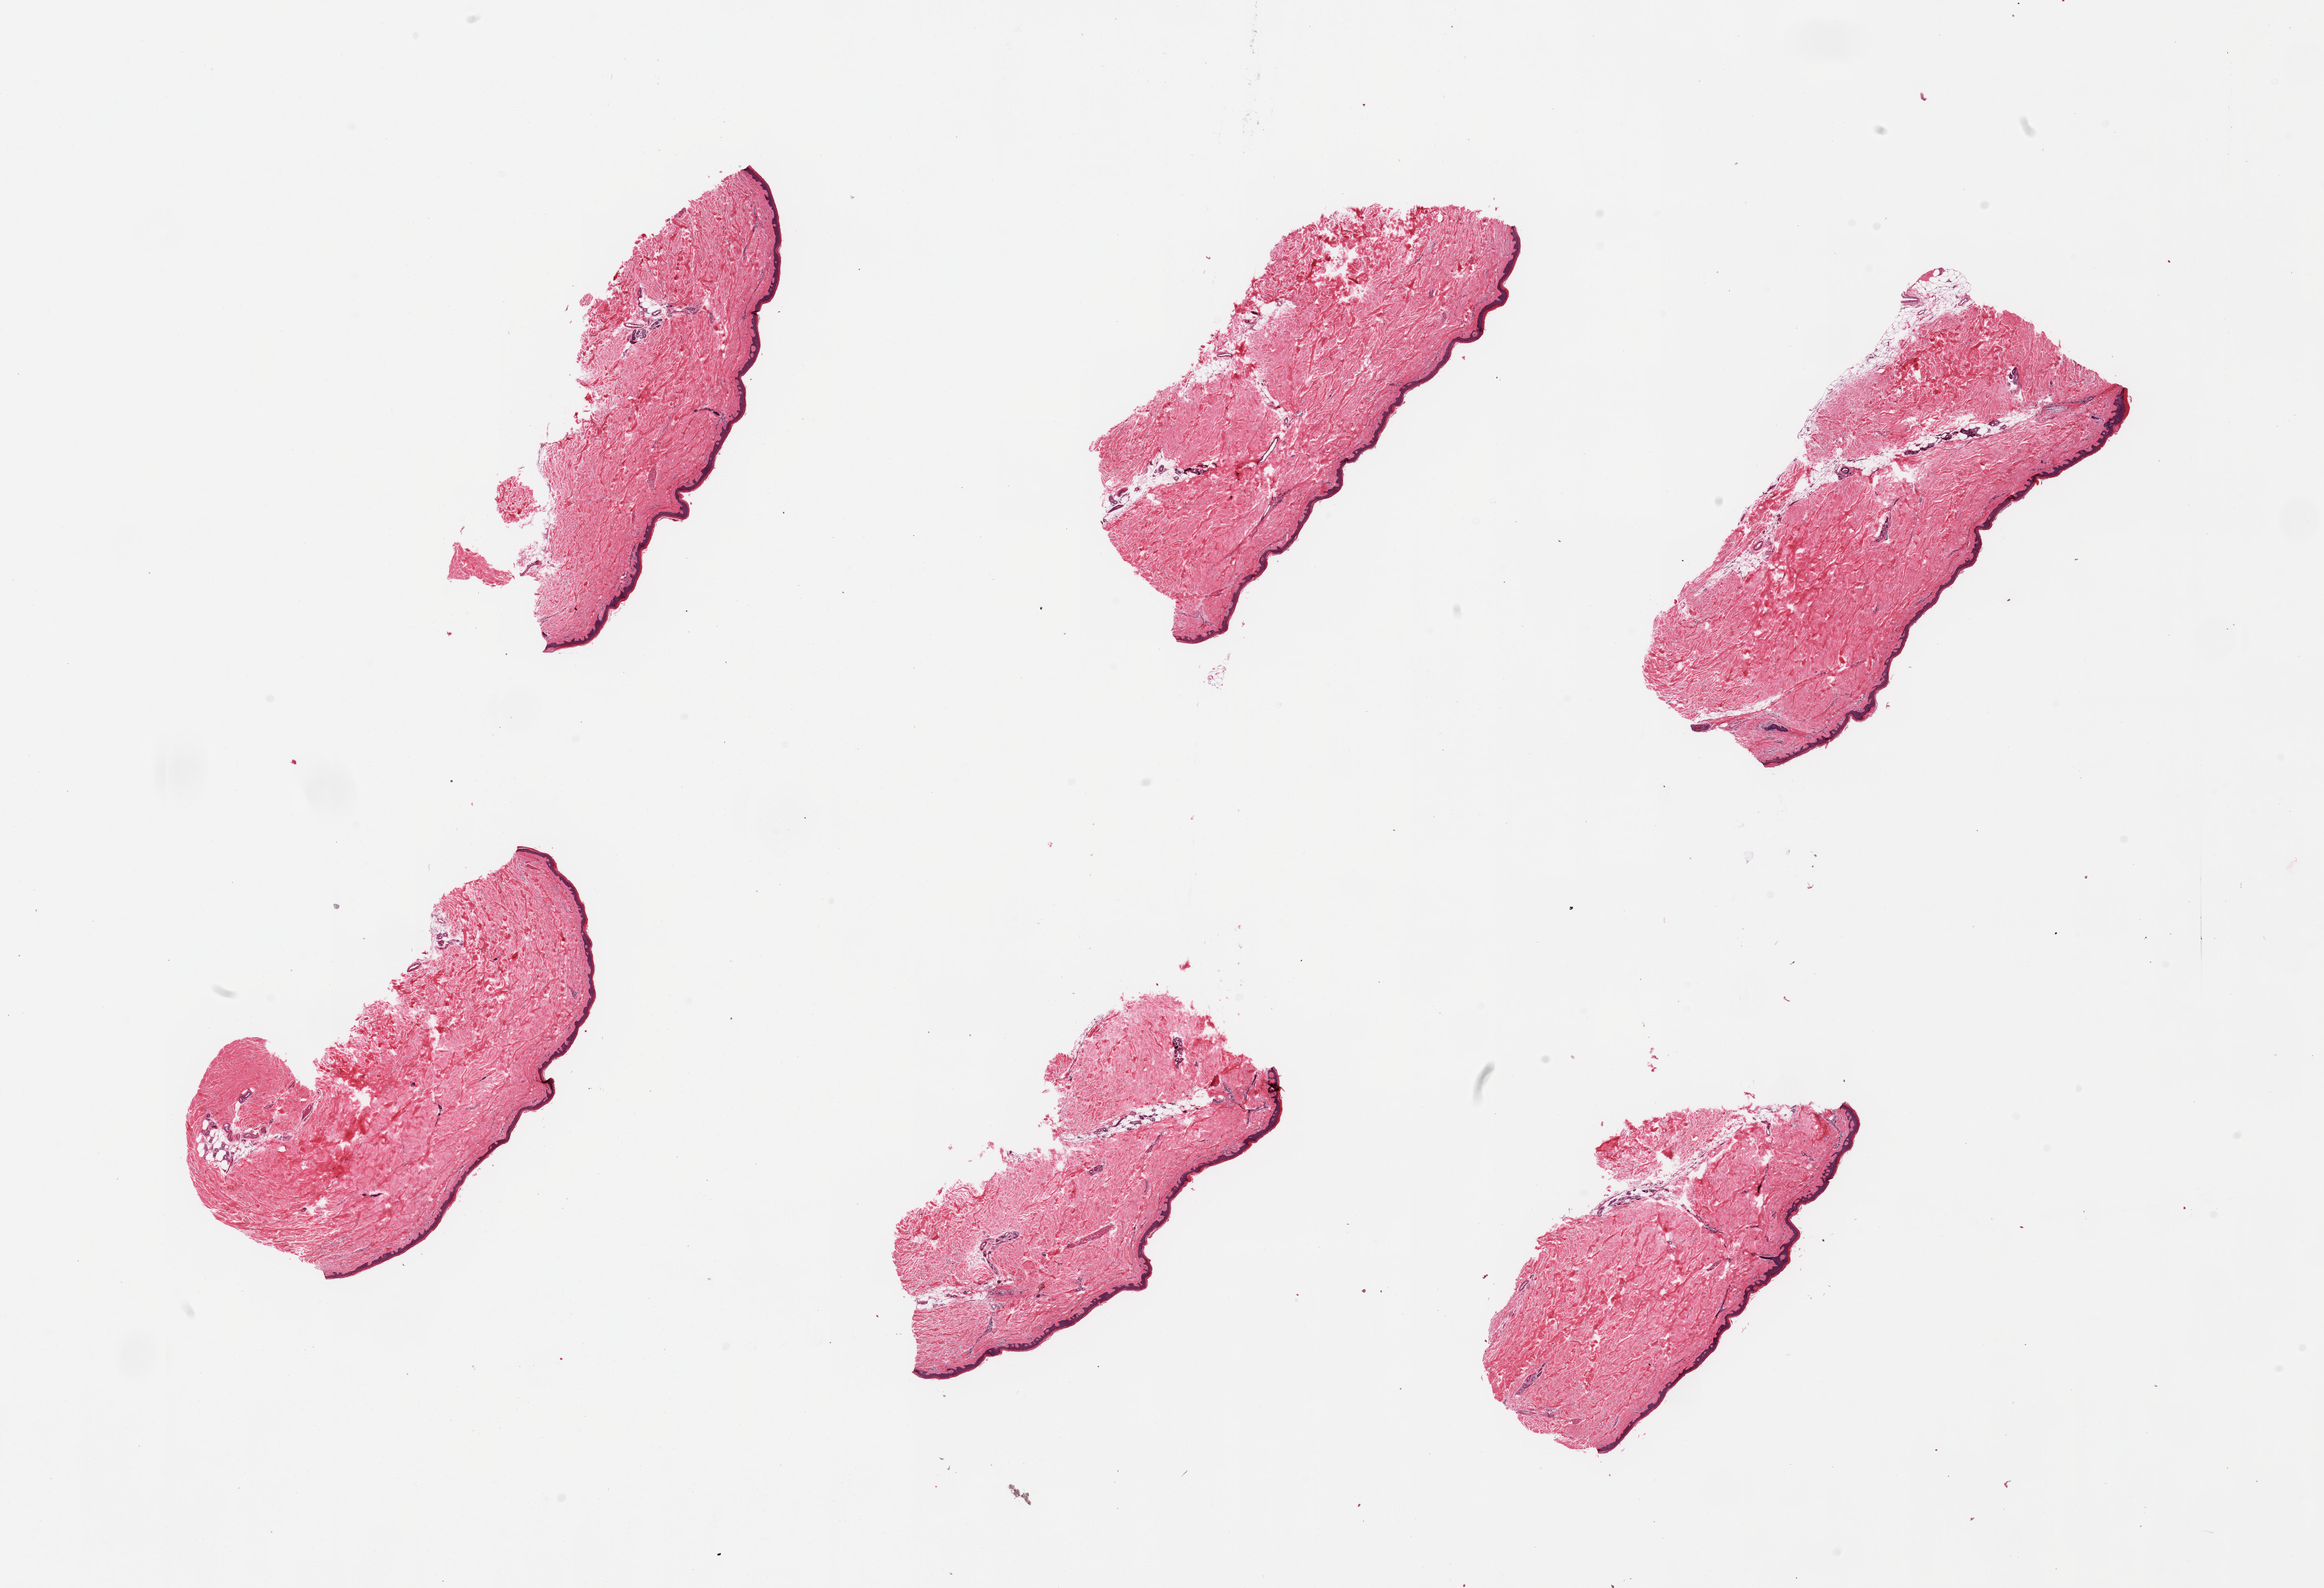
Digitized hematoxylin and eosin (H&E)-stained section, a low-resolution overview of the entire scanned area, about 27.6 x 18.8 mm (acquisition: 20x scan). PAXgene-fixed paraffin-embedded (PFPE) section. Section of skin of lower leg (target tissue). Donor tissue sample. Donor sex: male.
Pathologist's review note for this sample: 2 pieces; well trimmed, epidermis measures 33 microns.